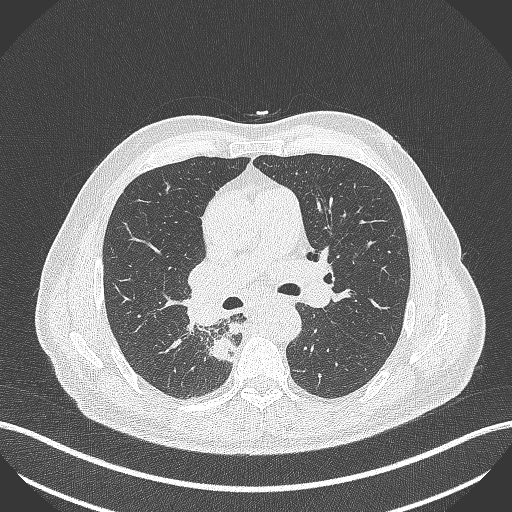
Chest CT, one axial slice; position 275 of 451 along the scan axis; lung window (W 1500 / L -600 HU); 1 mm slice thickness; 512 × 512 image matrix, field of view 400 × 400 mm. Patient: male, 61 years. Case-level facts recorded for this patient, not image findings: clinical TNM (as recorded): T1 N0 M0; histopathological grade: G3.
Annotated regions visible in this slice (rectangle marked by the reading radiologist):
- lung tumour (recorded histology: small cell carcinoma): bounding box (x1, y1, x2, y2) in pixels: (209, 333, 240, 366)